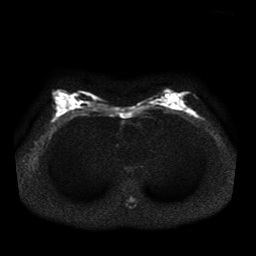
Breast MRI, one axial slice; slice 21 of 41 in the series (ordered by position); diffusion-weighted series; image 2 of 4 stored at this slice position (different b-values; order by instance number); 1.5 T; 5 mm slice thickness; 256 × 256 image matrix. Female patient.
Annotated regions visible in this slice (expert manual segmentation):
- tumour on diffusion-weighted imaging: bounding box [x1, y1, x2, y2] px = [188, 110, 194, 114]